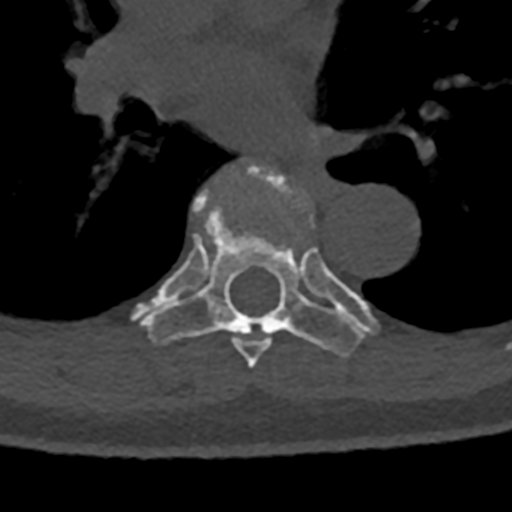
CT including the spine, one axial slice; position 777 of 797 along the scan axis; bone window (W 1800 / L 400 HU); 512 × 512 image matrix. Male patient, age 74 years. From the clinical record (not read from this slice): primary cancer: renal; vertebrae with lytic lesions (as recorded): T10, L1, L2, L3, L4, L5.
Outlined on this slice (semi-automatically segmented with operator editing):
- T6 vertebra: bounding box <179,171,299,368> (left, top, right, bottom; pixels)
- T7 vertebra: <132,180,376,357>